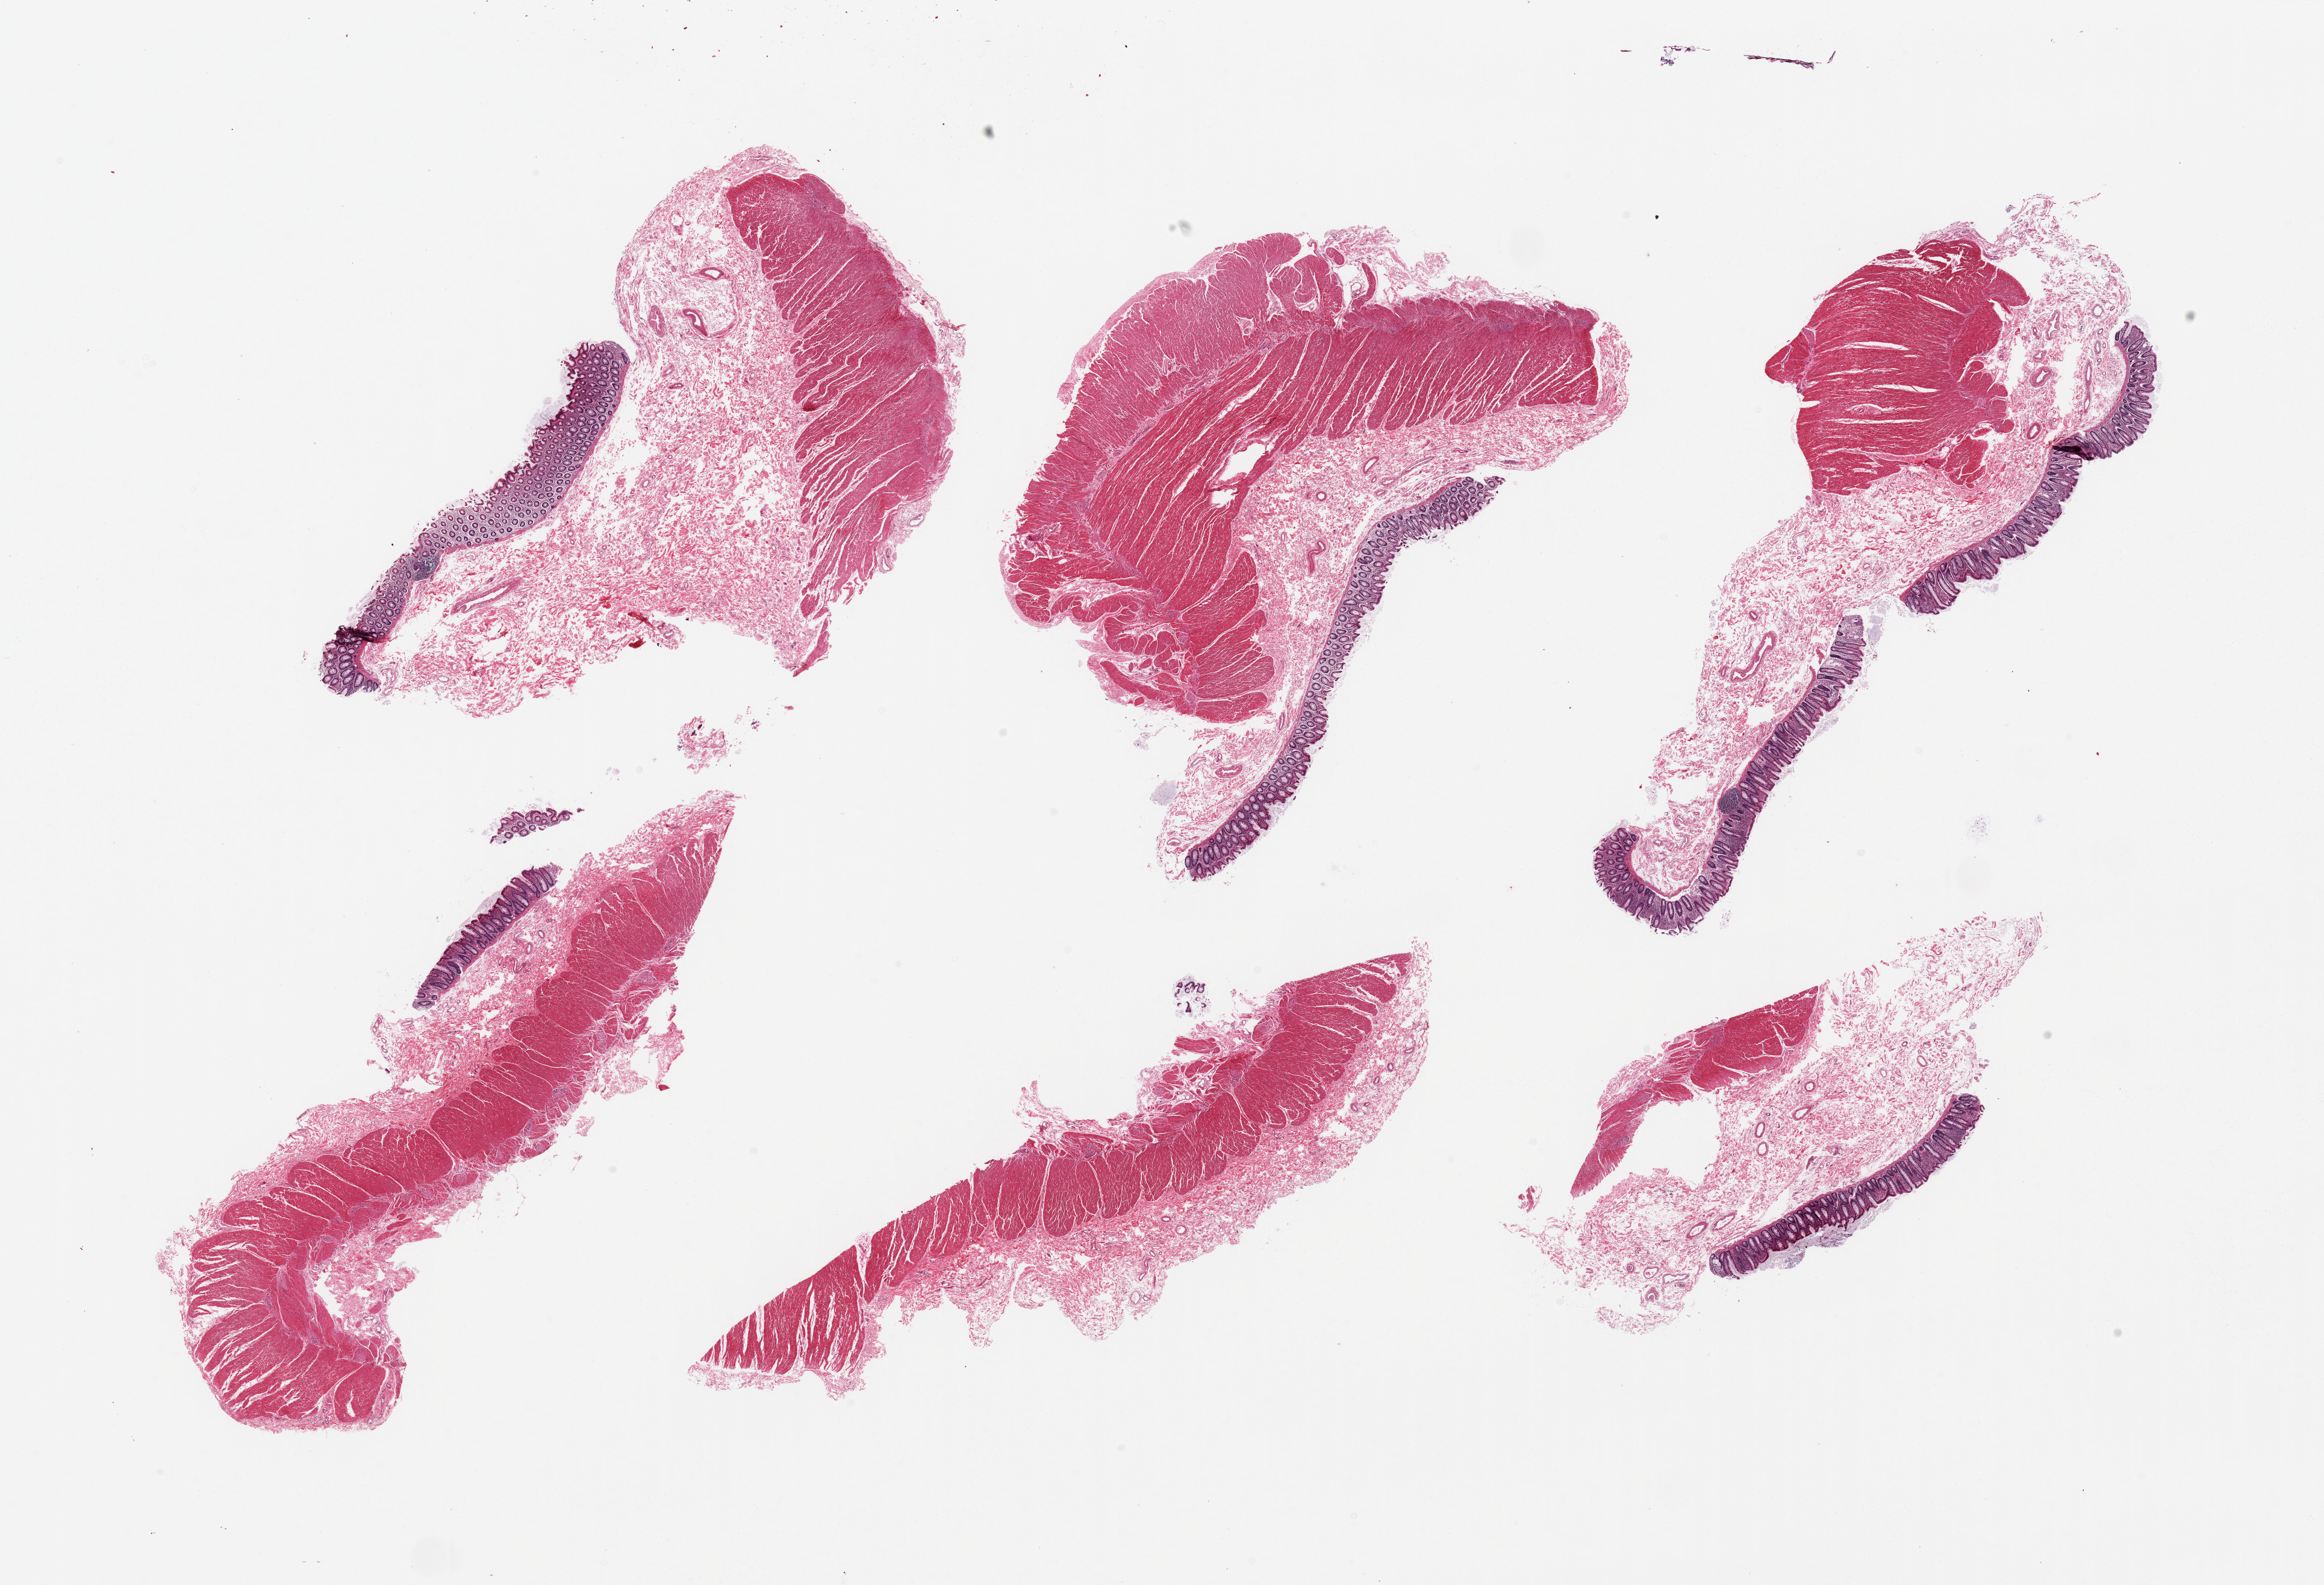
Digitized hematoxylin and eosin (H&E)-stained section, whole scanned area (about 30.5 x 20.8 mm, acquisition: 20x scan) shown as a low-resolution overview; PAXgene-fixed, paraffin-embedded tissue; sampled site (target tissue): transverse colon; donor tissue sample.
Review note (as recorded): 6 pieces, 1 without mucosa.